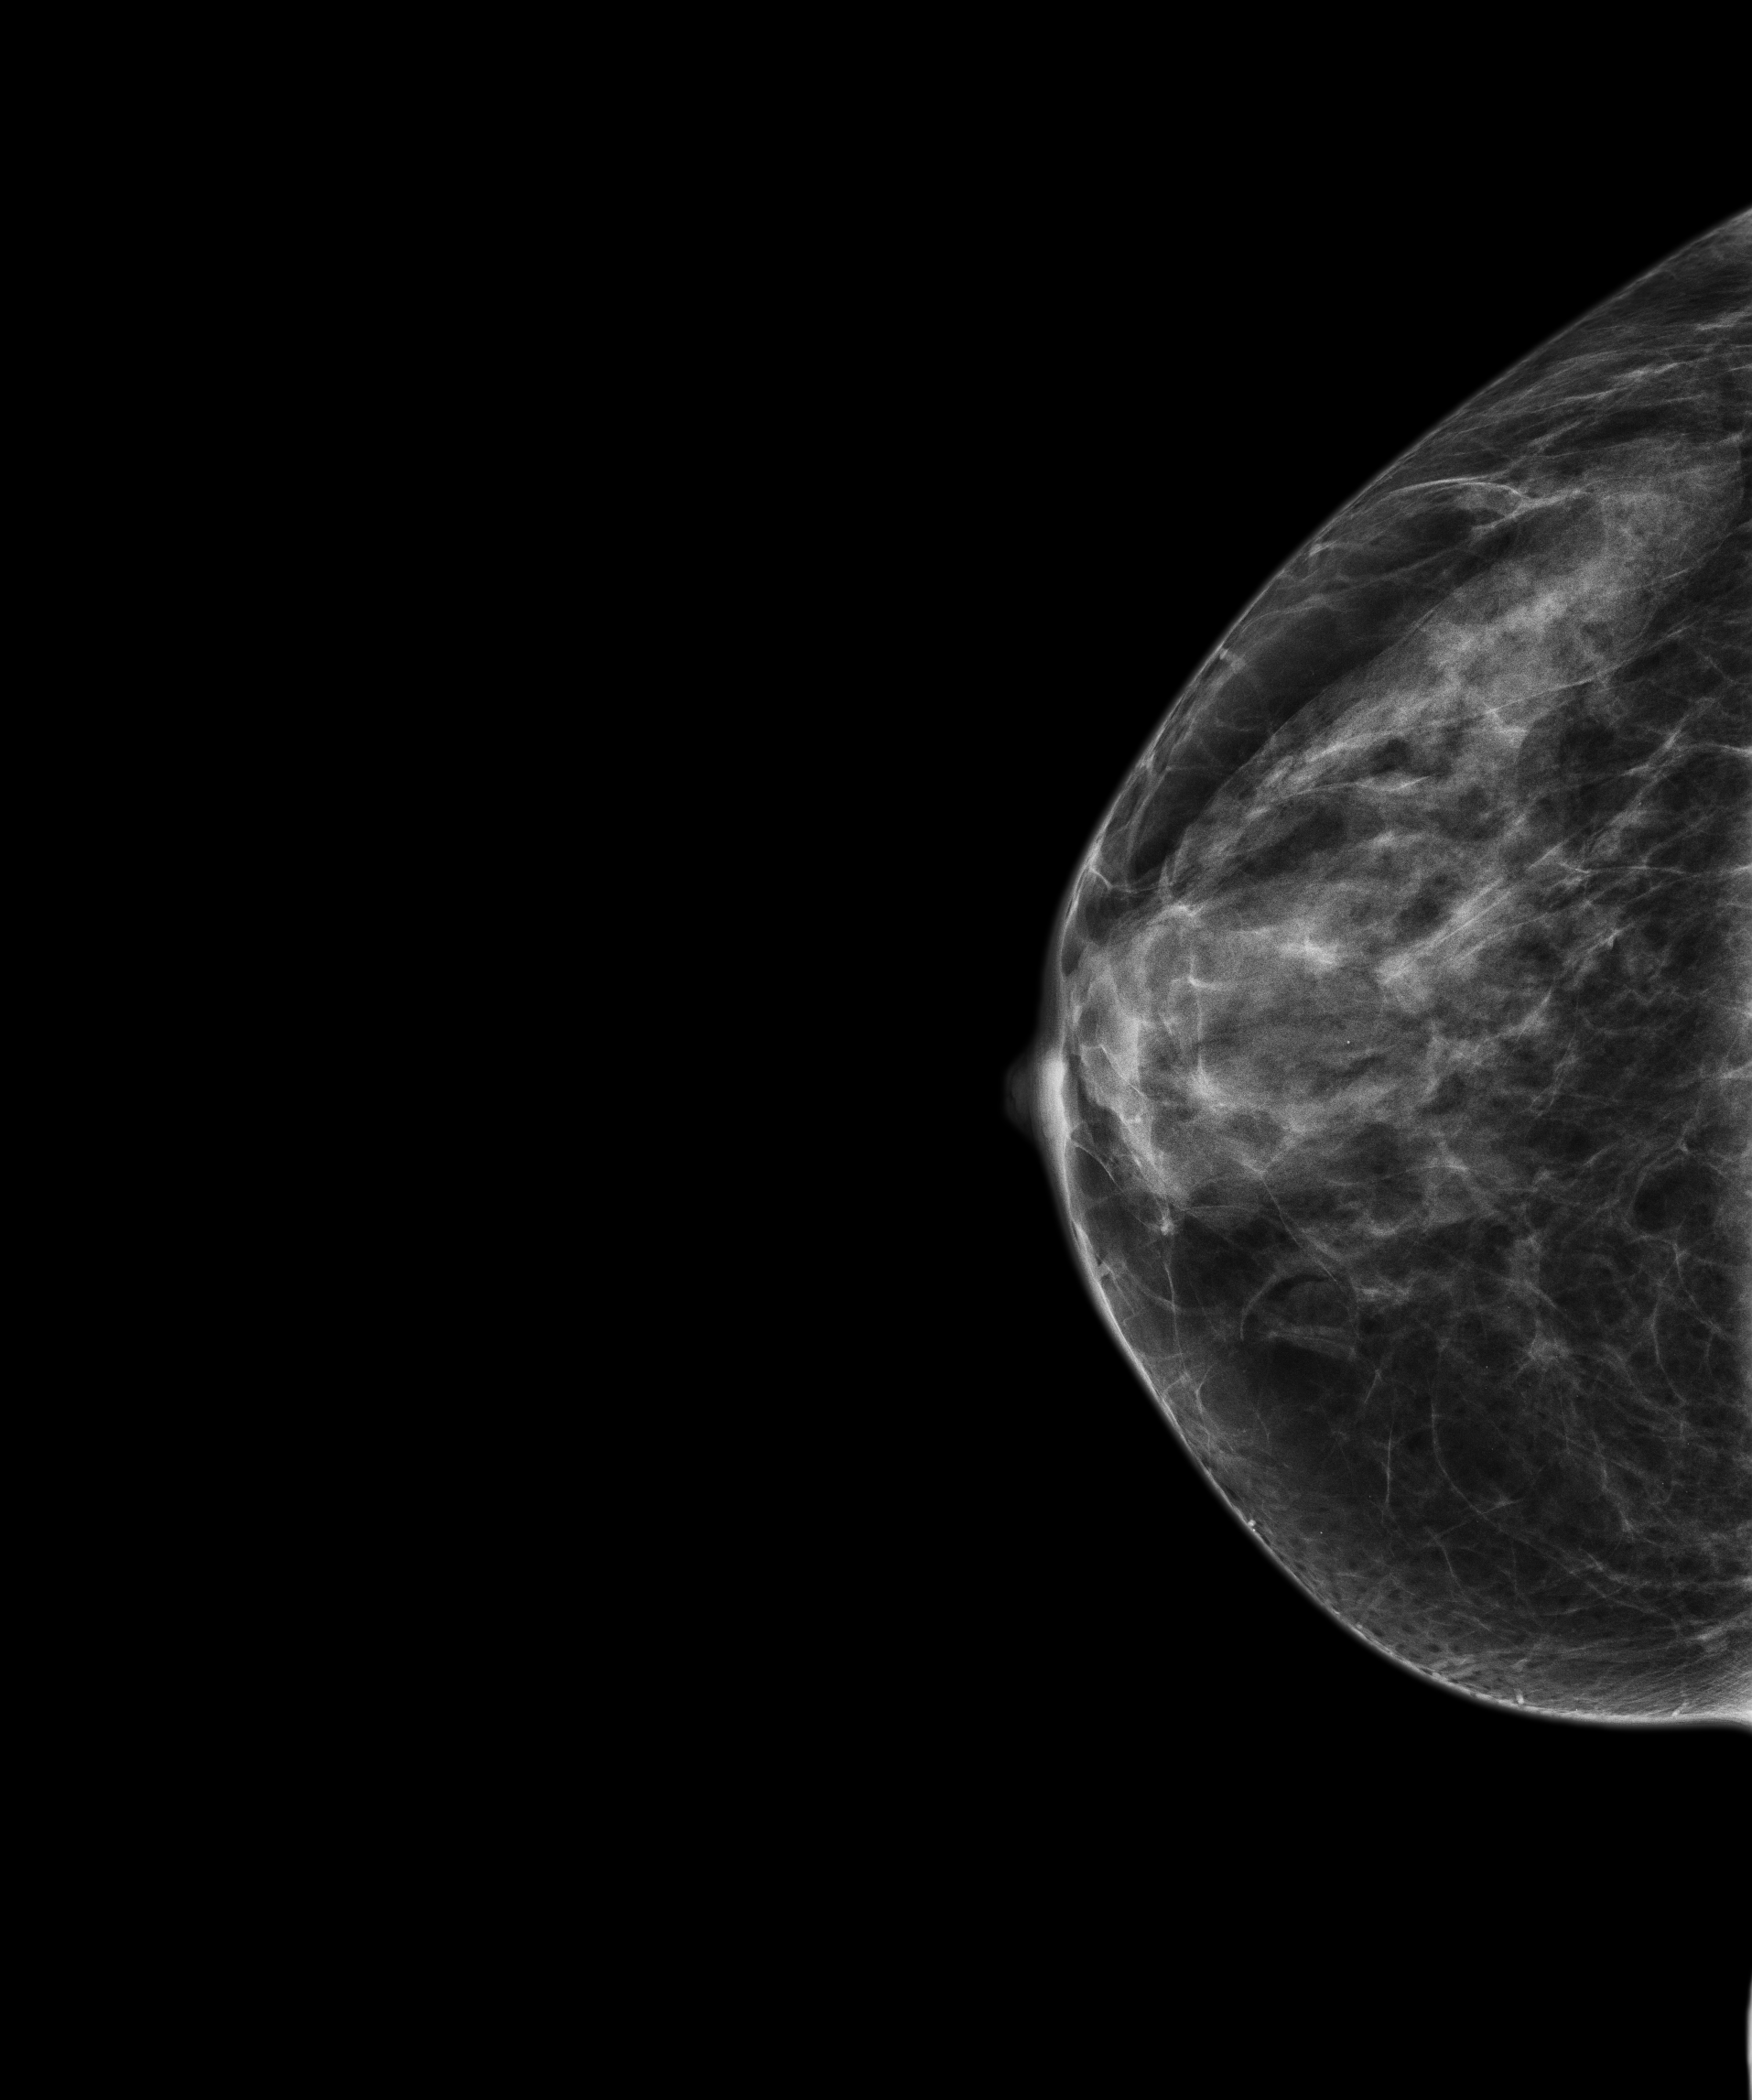
Screening examination; compressed breast thickness 33.7 mm; system: Senographe Pristina. Patient: female, 49 years.
Image type: full-field digital mammogram. Breast: right. Projection: craniocaudal (CC) view.